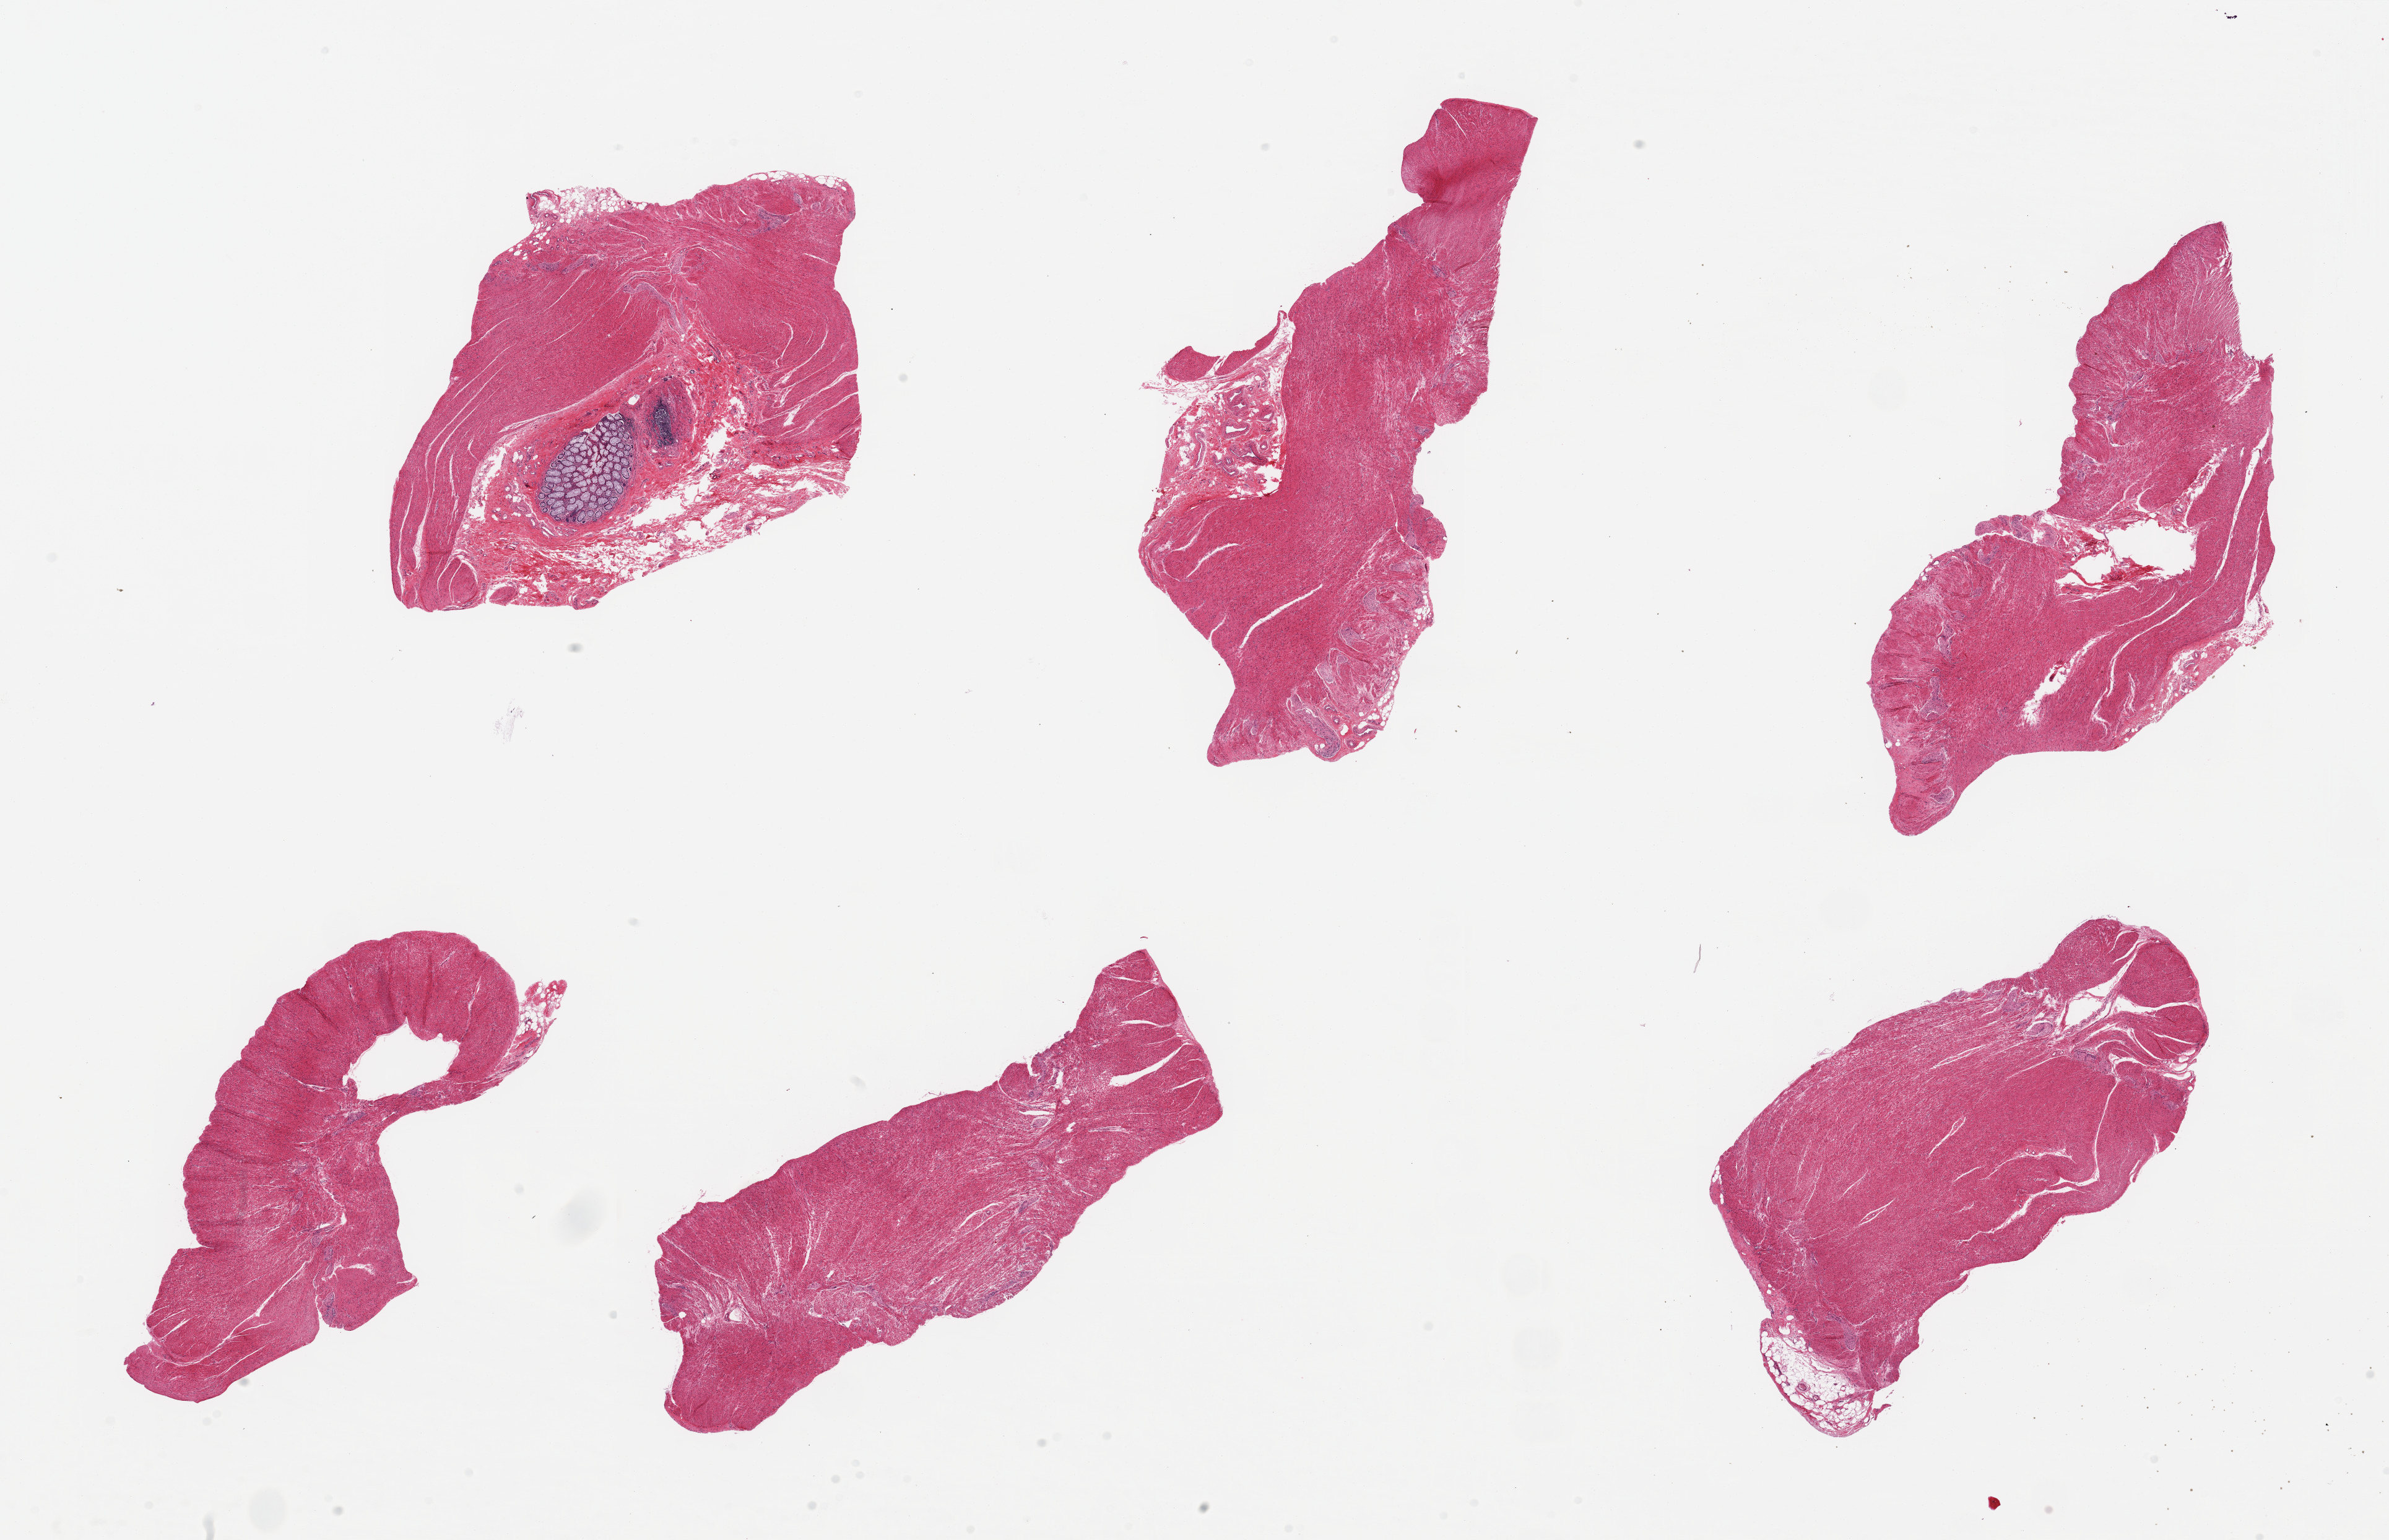
Digitized haematoxylin and eosin-stained section, brightfield — low-resolution overview of the scanned area, about 30.5 x 19.7 mm (slide scanned at 20x). PAXgene-fixed, paraffin-embedded tissue. Sampled site (target tissue): sigmoid colon. Donor tissue sample. Donor sex: male.
Review note (as recorded): 6 pieces, up to 9x4mm; `90+% muscle, trace mucosa, fat present.